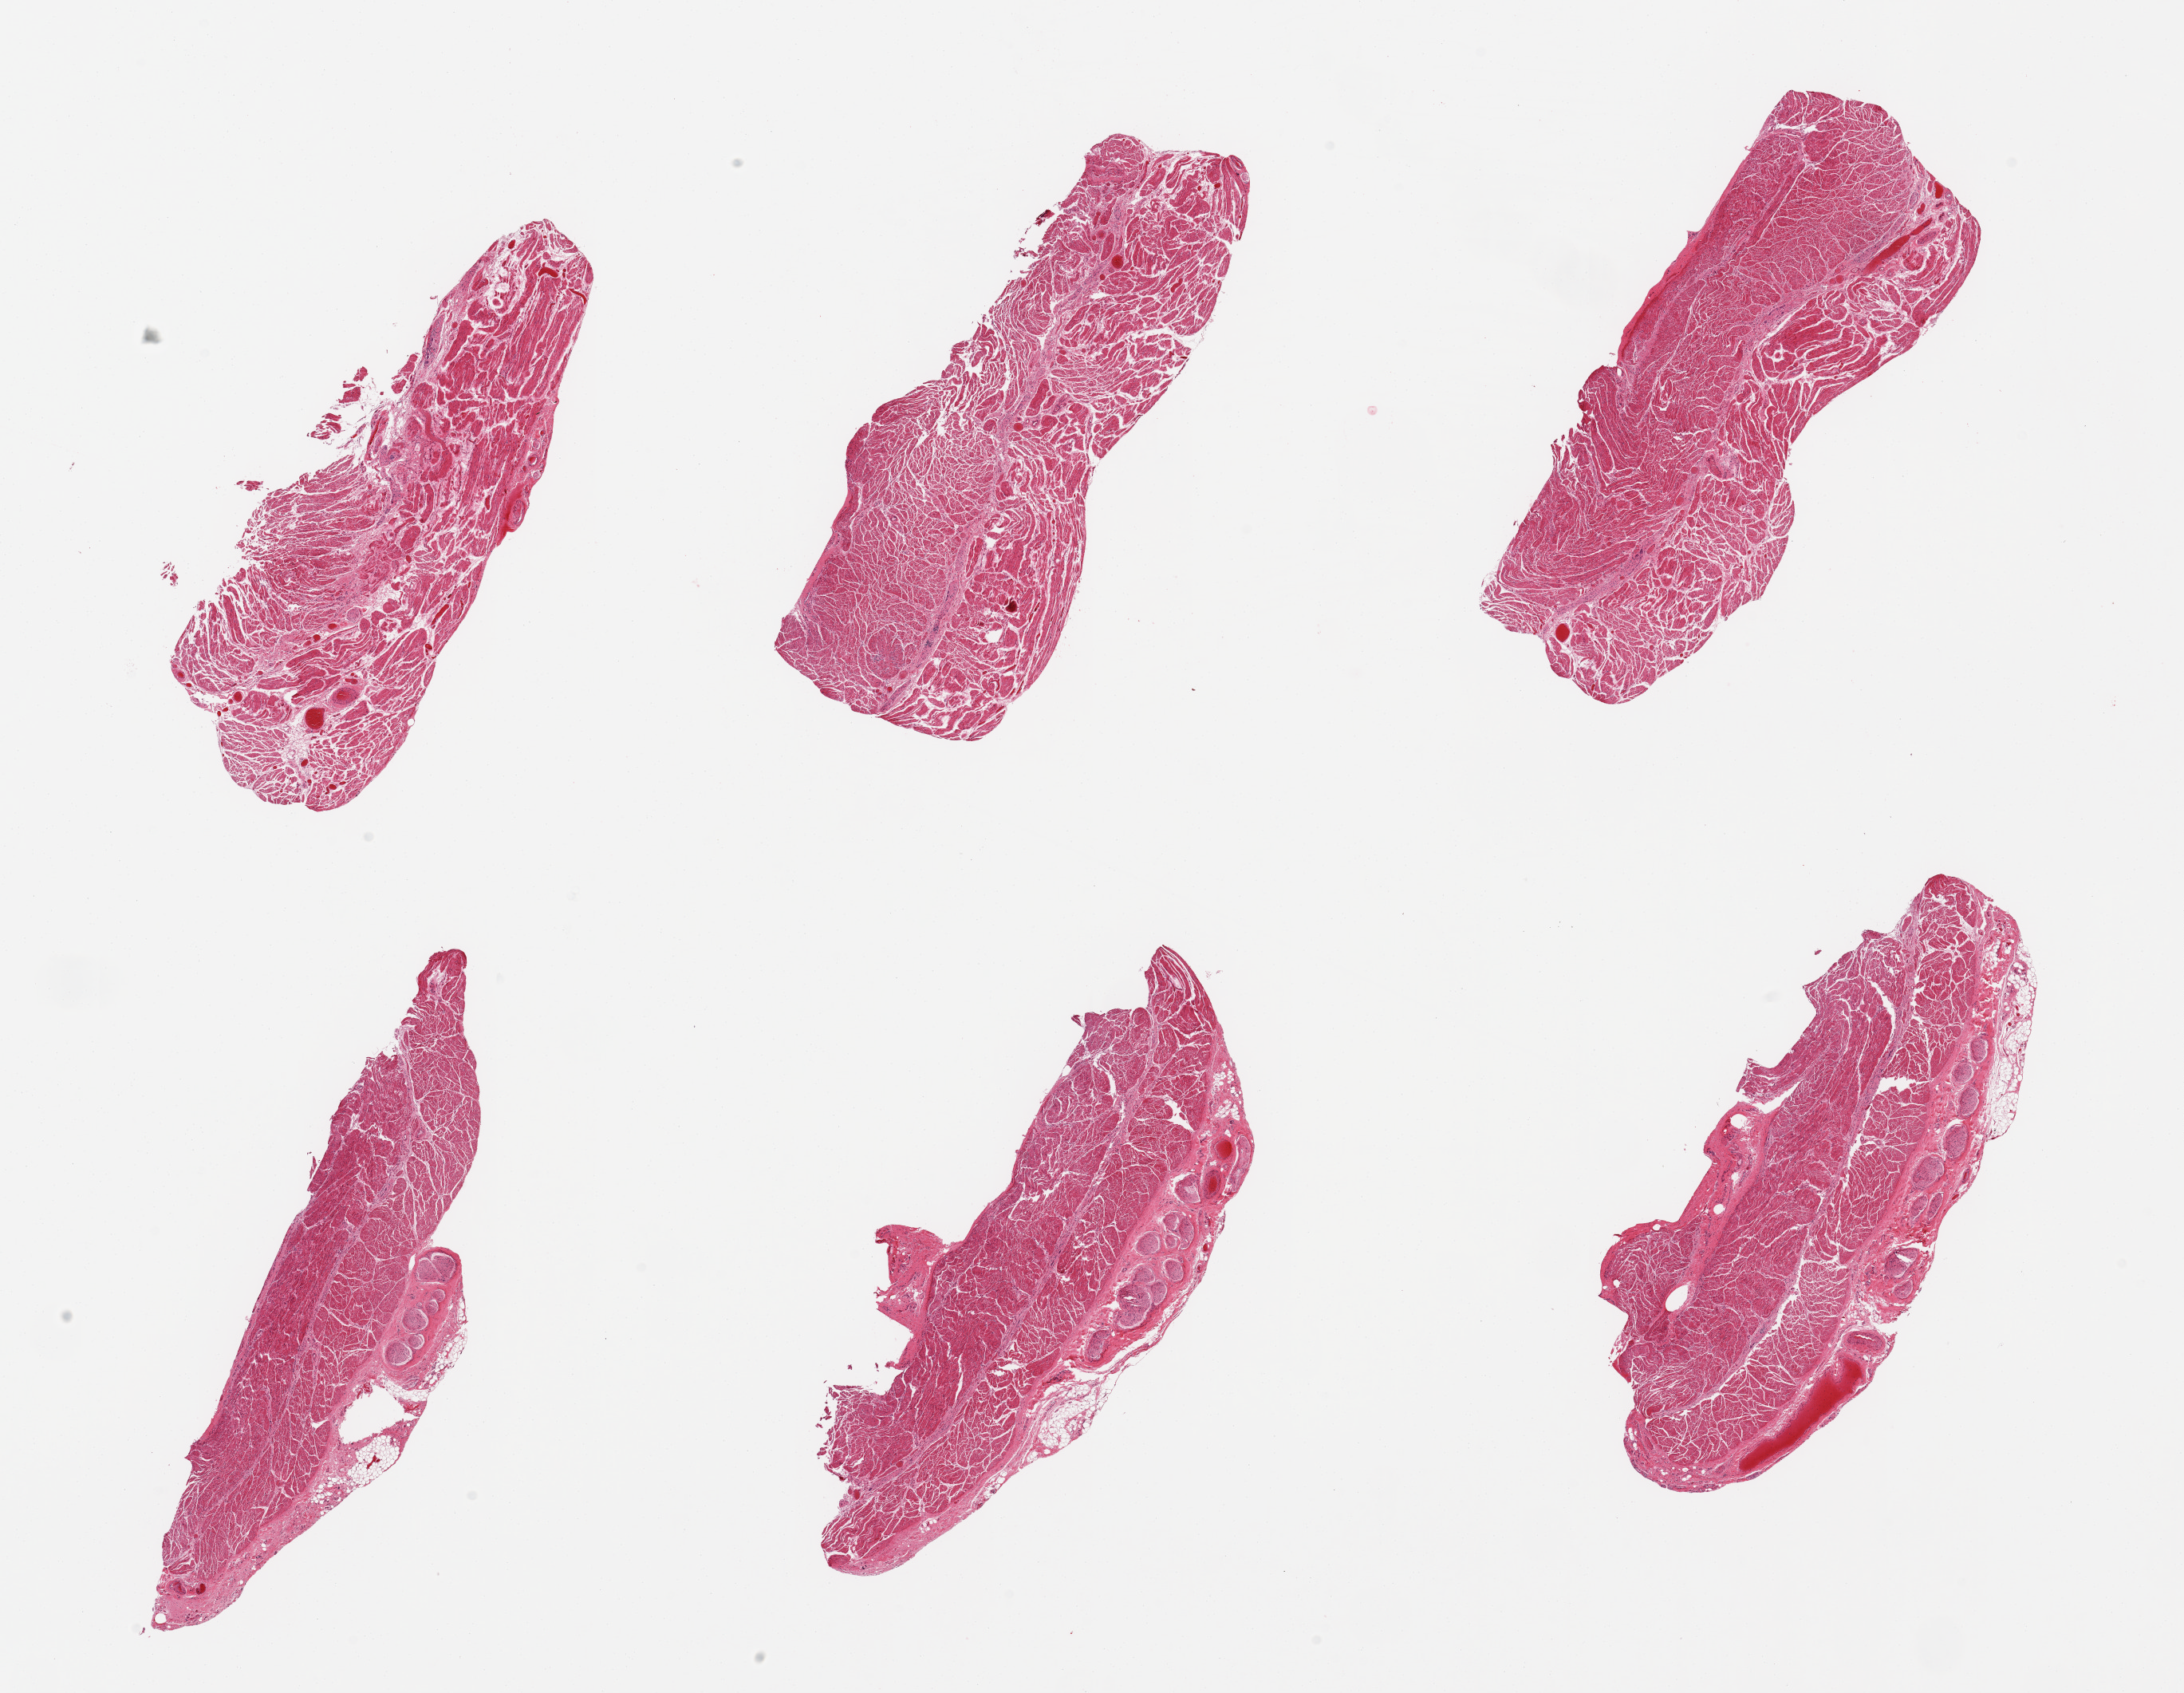
Digitized H&E-stained section, brightfield, whole scanned area (about 21.7 x 16.8 mm, slide scanned at 20x) shown as a low-resolution overview, PAXgene-fixed paraffin-embedded (PFPE) section, section of esophageal muscle (target tissue), tissue donor sample. Donor: female.
• reviewer comment on this tissue sample: 6 pieces; nerves in adventitia of 3 pieces comprise 10%; well dissected